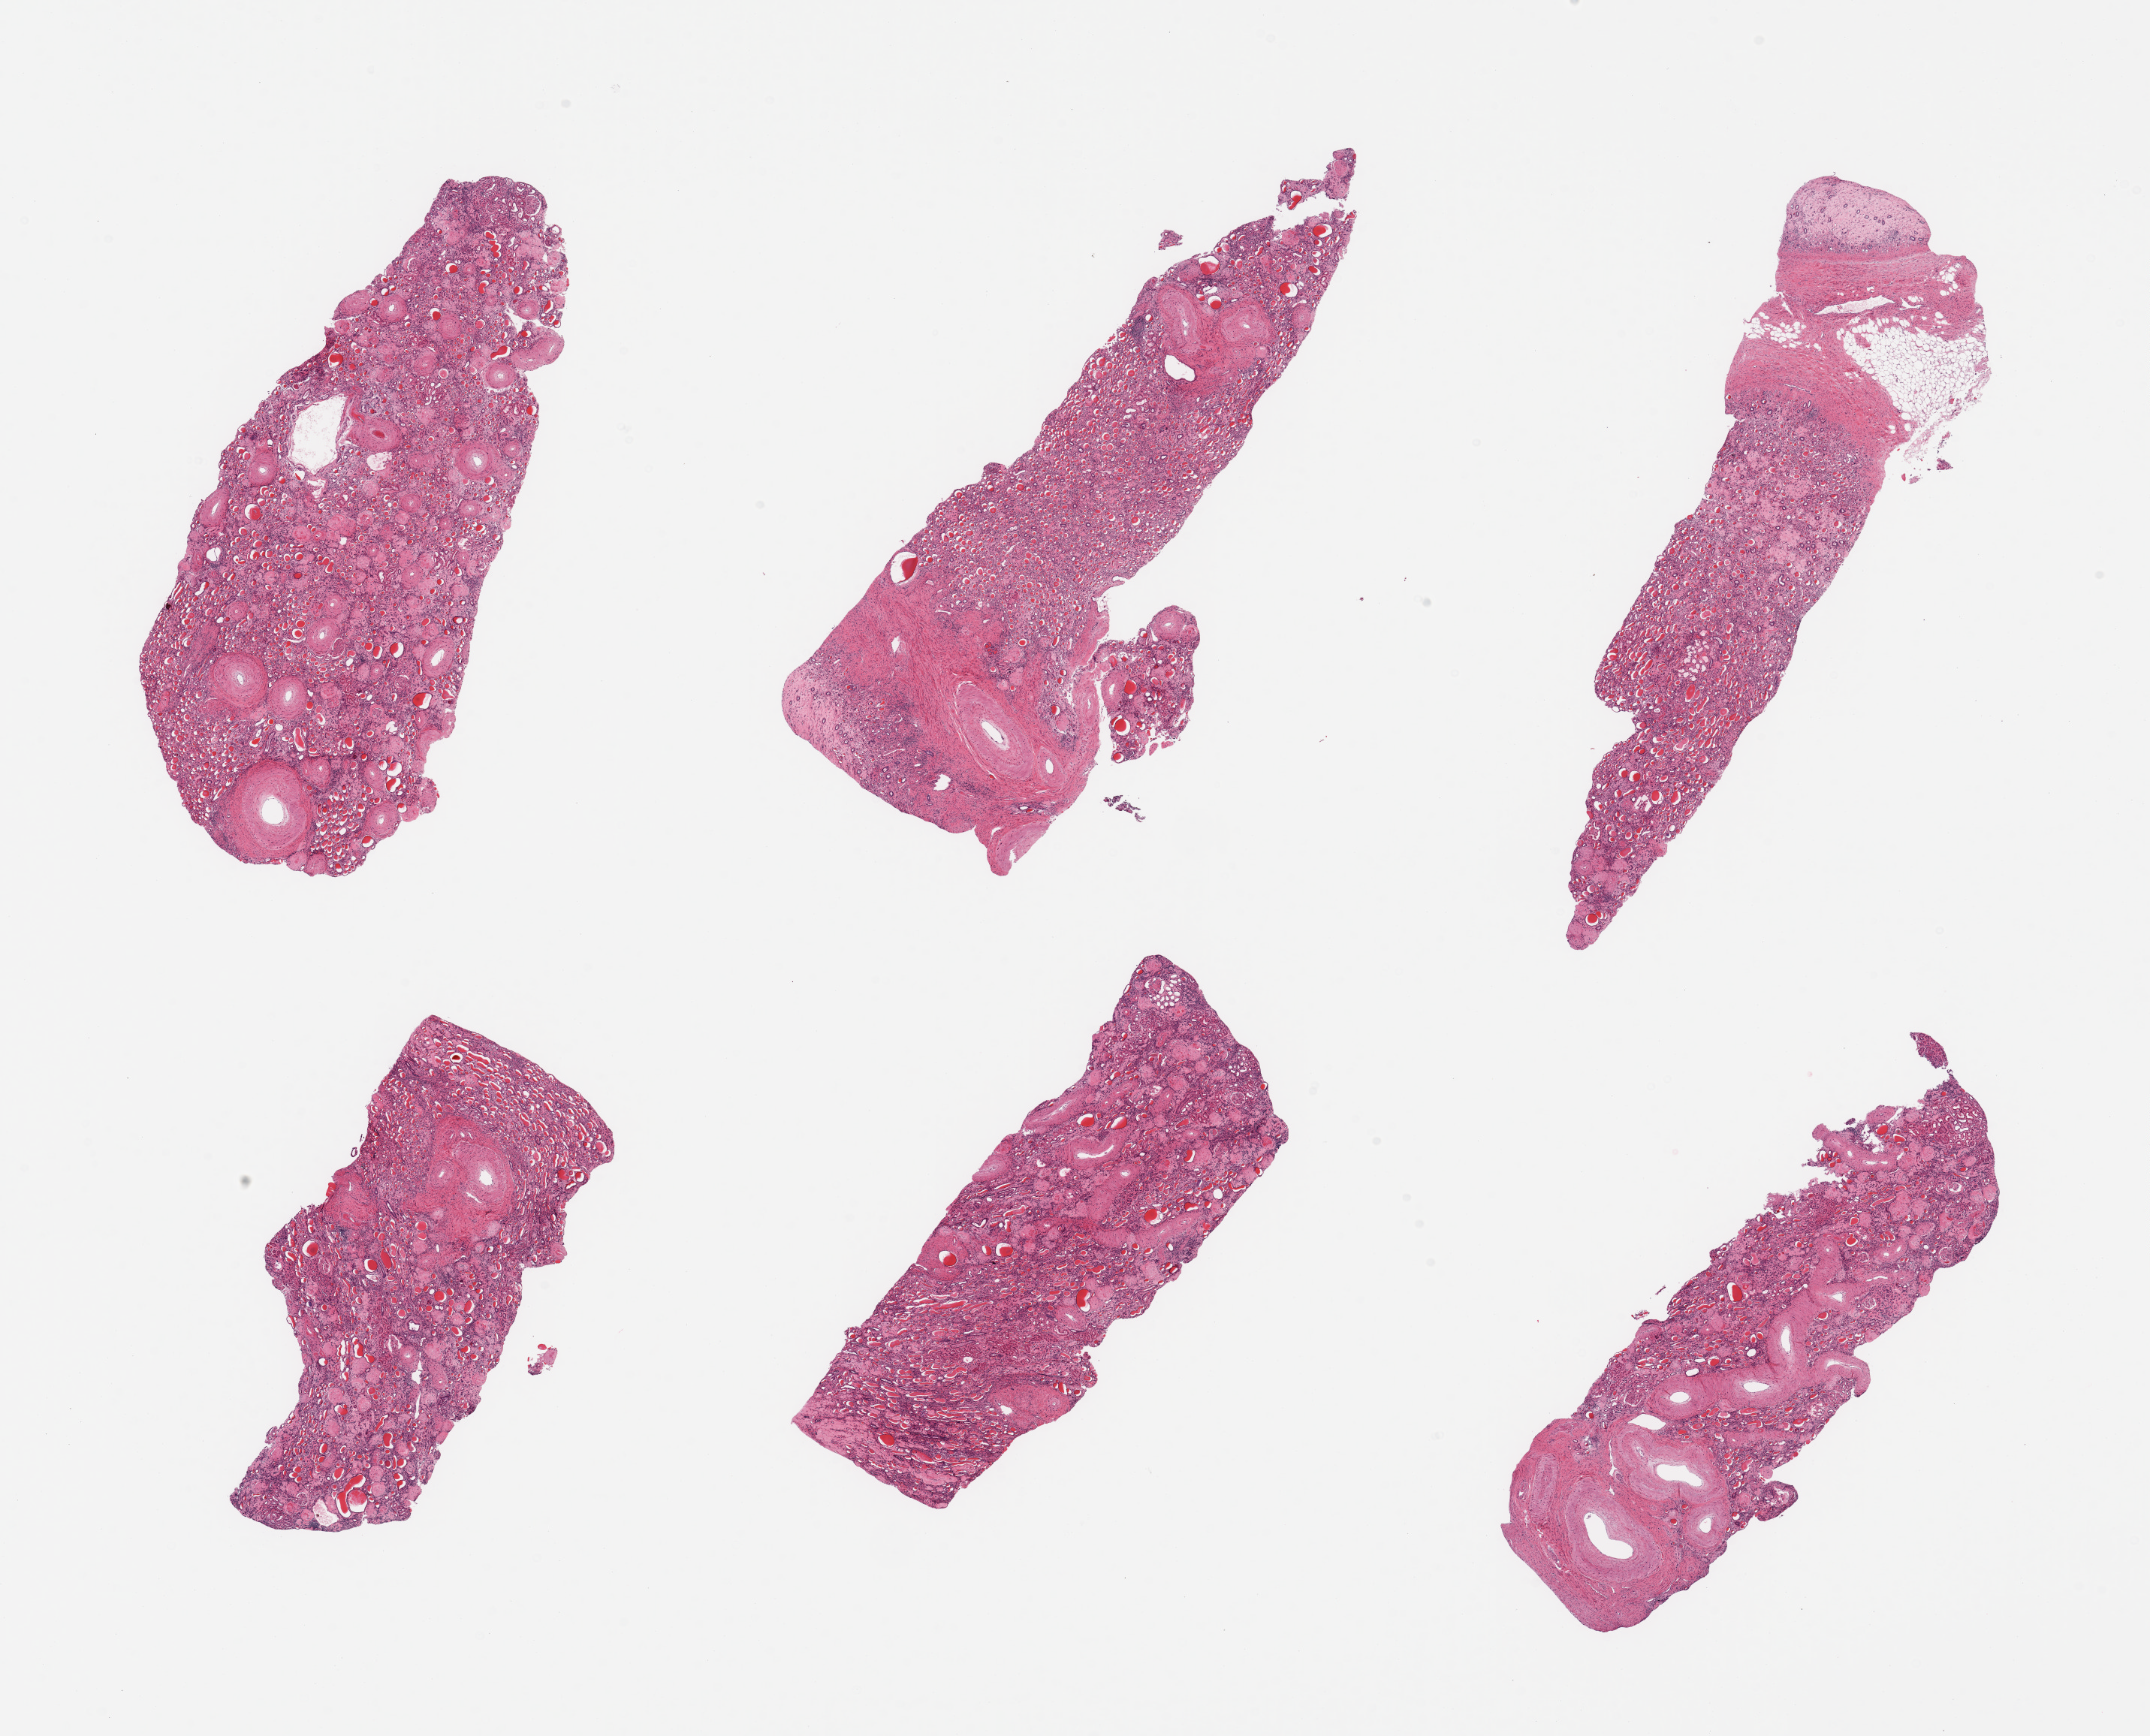
Whole-slide image, H&E stain, brightfield, whole scanned area (about 22.6 x 18.3 mm) shown as a low-resolution overview. PAXgene-fixed, paraffin-embedded tissue. Target tissue: renal cortex. Donor tissue sample. Donor: male.
Reviewer comment on this tissue sample: 6 pieces; severe arterial, arteriolar, & glomerular sclerosis with extensive tubular hyalin casts; no normal tissue remains.